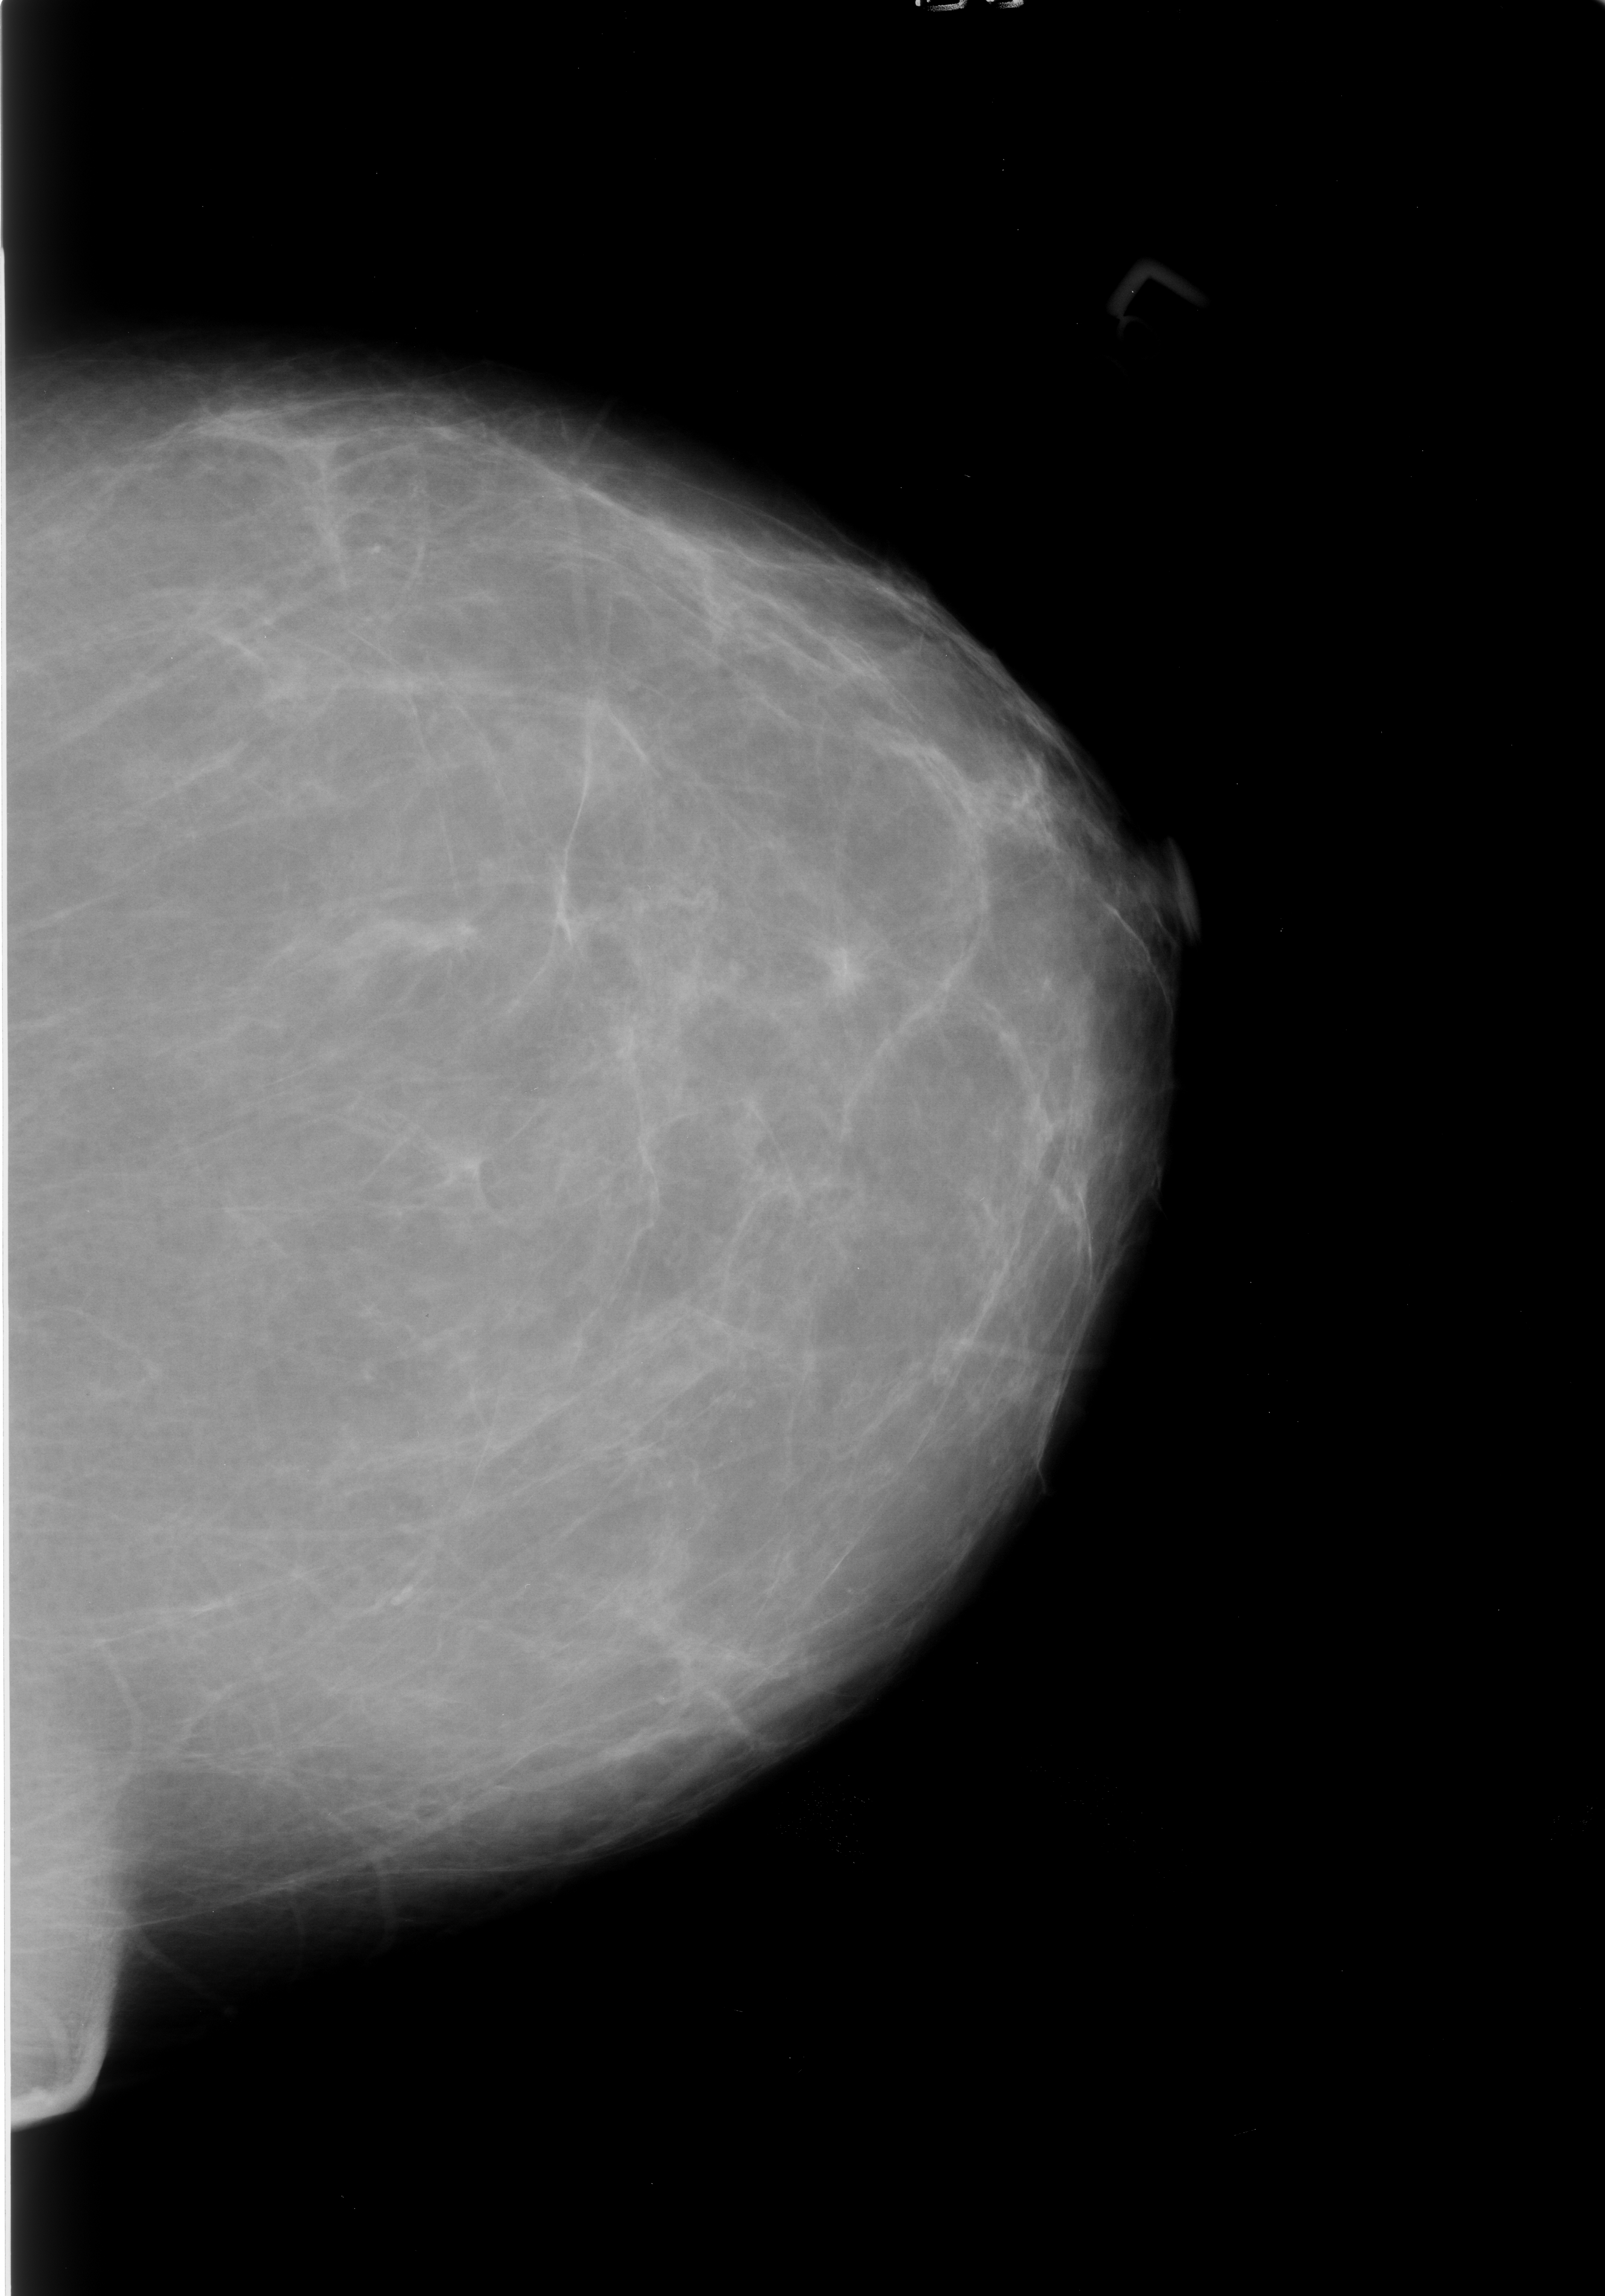
Mammogram (digitized film). Left breast. Craniocaudal (CC) view. 1605 × 2296 image matrix.
Expert-marked regions of interest on this film, with their recorded descriptors:
- mass, shape irregular / architectural distortion, margins spiculated; BI-RADS assessment category 4; pathology result (as recorded, not read from the image): malignant: bounding box [x1, y1, x2, y2] px = [802, 920, 885, 1010]